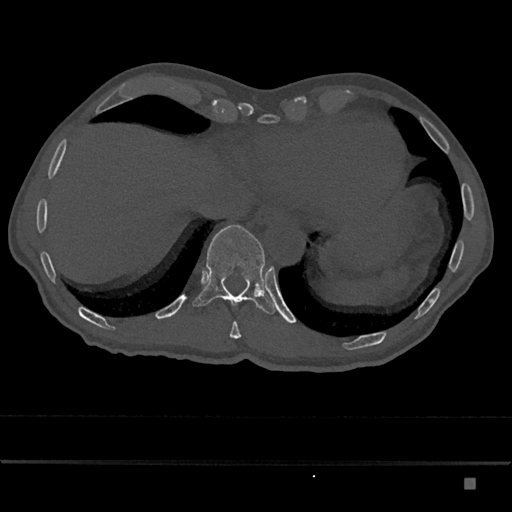
CT including the spine, one axial slice; position 692 of 797 along the scan axis; reconstruction kernel Br40s/3; bone window (W 1800 / L 400 HU); 512 × 512 image matrix, field of view 390 × 390 mm. Male patient, age 72 years. From the clinical record (not read from this slice): primary cancer: prostate.
Annotated regions visible in this slice (semi-automatic segmentation, software-assisted and operator-edited):
- T10 vertebra: bounding box (x1, y1, x2, y2) in pixels: (229, 321, 241, 339)
- T11 vertebra: (192, 225, 275, 314)